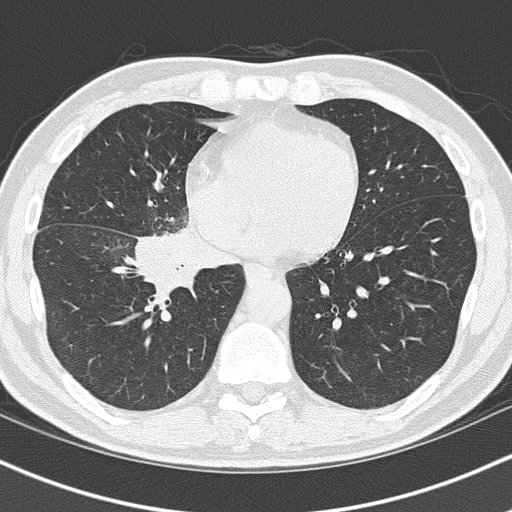
Low-dose screening chest CT, one axial slice. Position 49 of 151 along the scan axis. Reconstruction kernel B50f. 120 kVp. Lung window (W 1500 / L -600 HU). 2 mm slice thickness. 512 × 512 image matrix.
Structures marked on this image (outlined manually by an expert reader):
- lesion 1 (tumor, hilum of right lung): bounding box (x1, y1, x2, y2) in pixels: (137, 234, 201, 290)